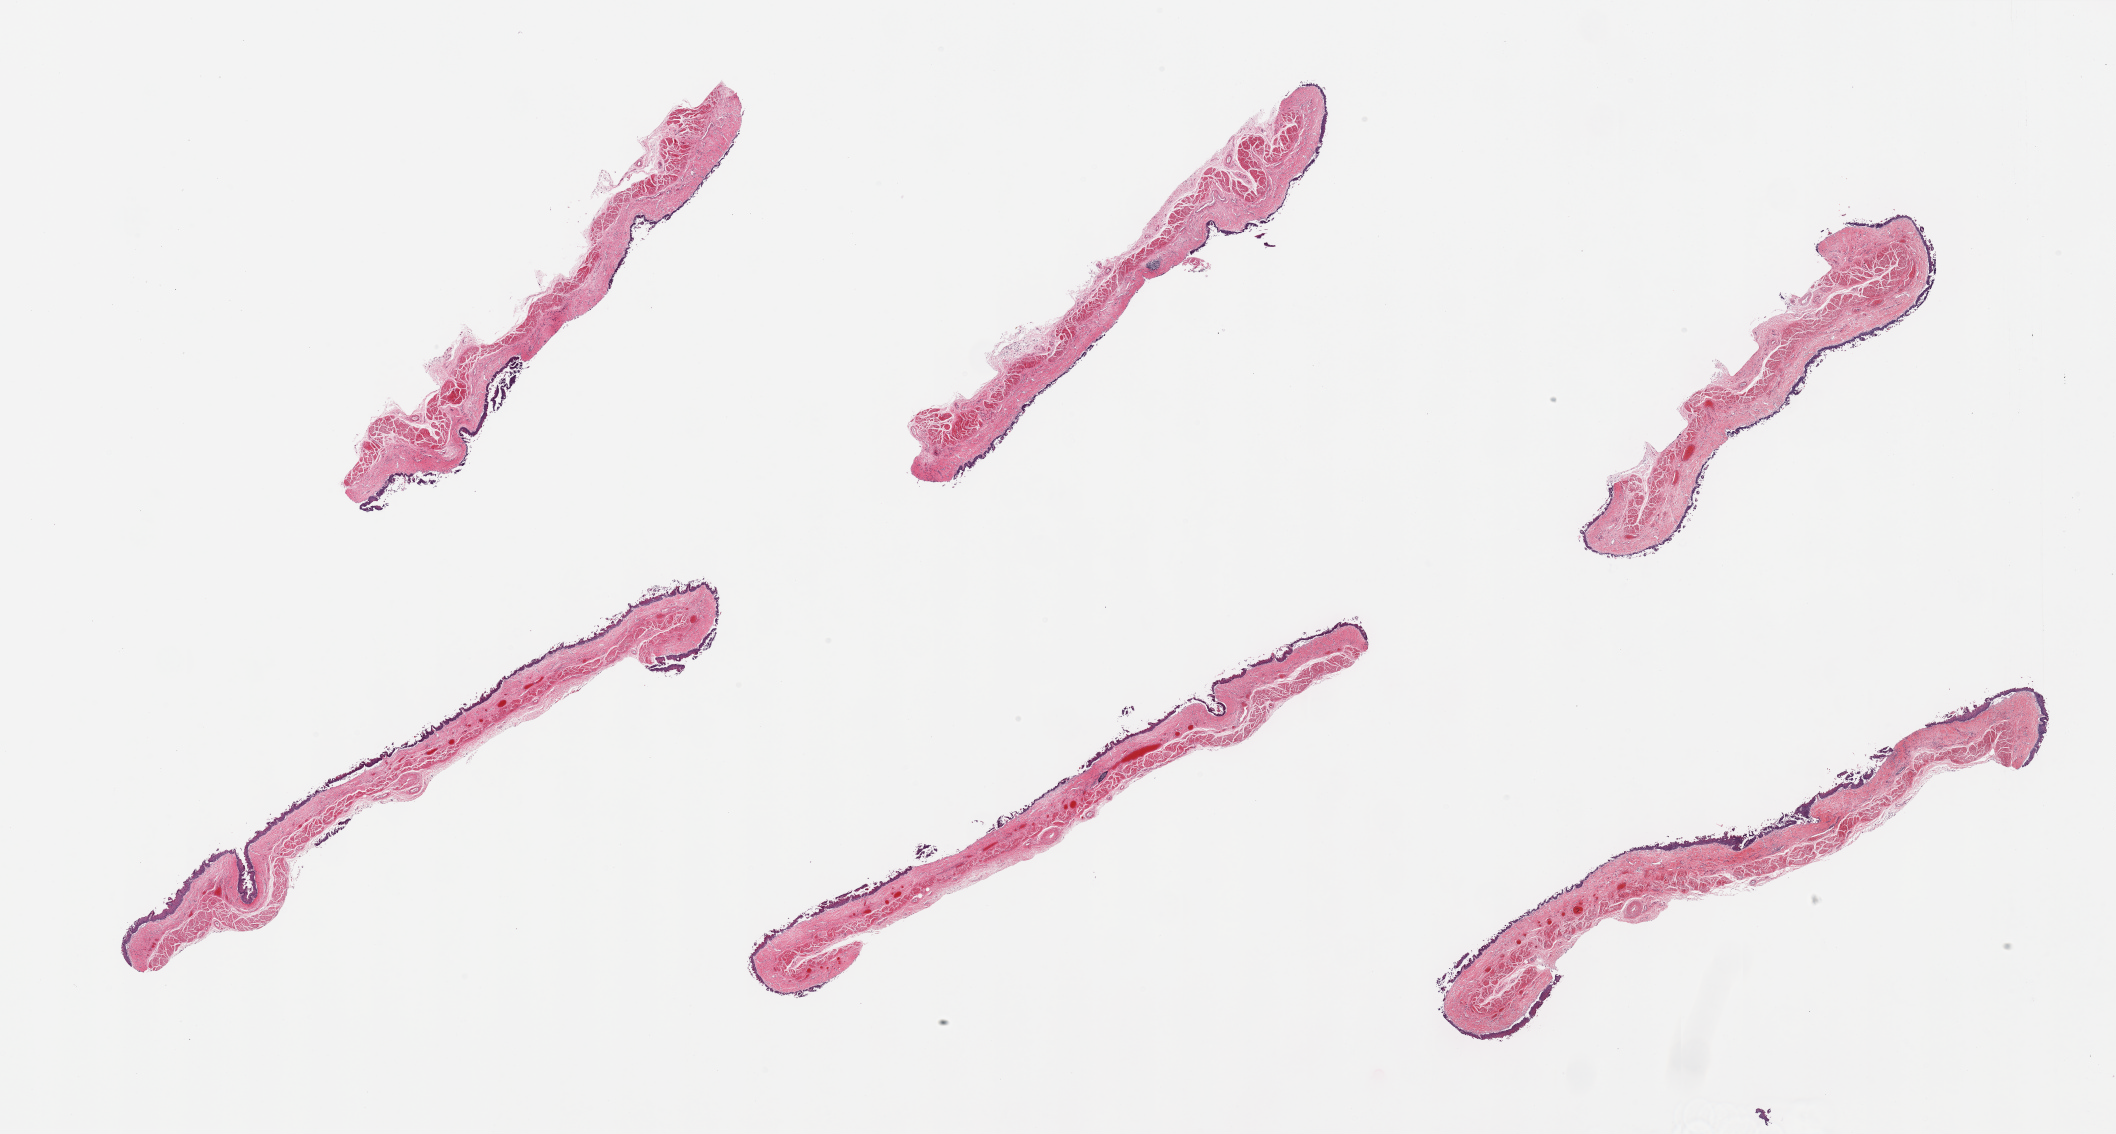
Digitized hematoxylin and eosin (H&E)-stained section, brightfield, whole scanned area (about 33.5 x 17.9 mm) shown as a low-resolution overview. PAXgene-fixed paraffin-embedded (PFPE) section. Target tissue: esophageal mucous membrane. Tissue donor sample. Donor: female.
* reviewer comment on this tissue sample: 6 pieces, squamous mucosa sloughling, unusually poorly preserved, residual basal portions less than ~0.1mm